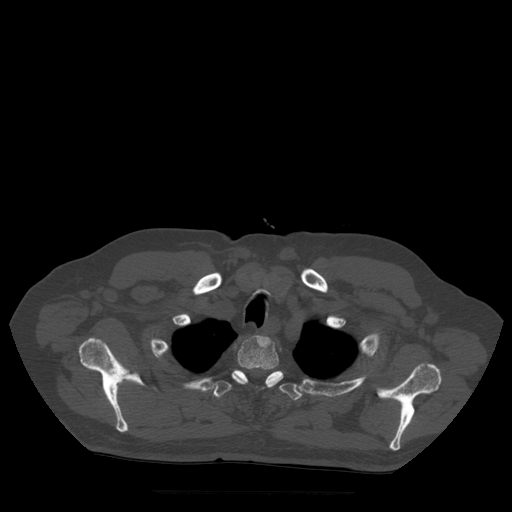
CT including the spine, one axial slice. Position 419 of 522 along the scan axis. Bone window (W 1800 / L 400 HU). 1.25 mm slice thickness. 512 × 512 image matrix, field of view 420 × 420 mm. Patient age 72 years. Case-level facts recorded for this patient, not image findings: primary cancer: prostate.
Annotated regions visible in this slice (semi-automatic segmentation, software-assisted and operator-edited):
- T2 vertebra: bounding box [x1, y1, x2, y2] px = [232, 336, 284, 390]
- T3 vertebra: [213, 371, 303, 401]